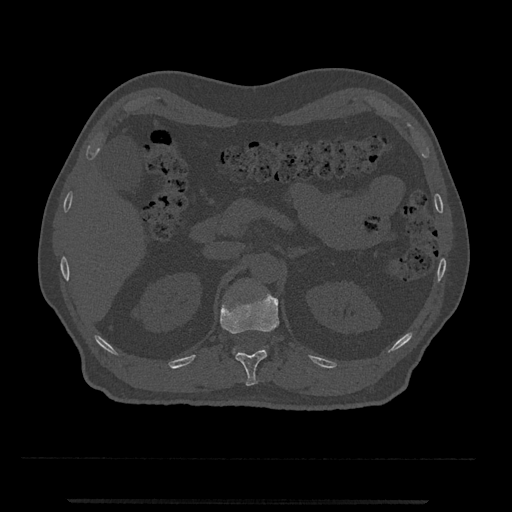
CT including the spine, one axial slice; slice 381 of 797 in the series (ordered by position); 120 kVp; bone window (W 1800 / L 400 HU); 0.5 mm slice thickness; 512 × 512 image matrix, field of view 419 × 419 mm. Patient: male, 63 years. Case-level facts recorded for this patient, not image findings: primary cancer: prostate.
Annotated regions visible in this slice (semi-automatically segmented with operator editing):
- L1 vertebra: bounding box (x1, y1, x2, y2) in pixels: (233, 349, 236, 353)
- T12 vertebra: (220, 292, 280, 386)